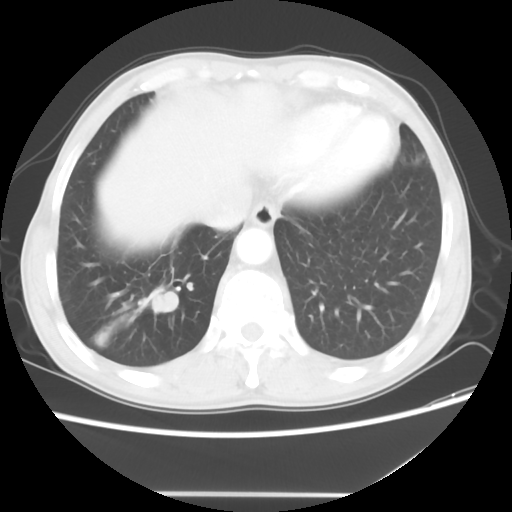
Chest CT, one axial slice; slice 10 of 56 in the series (ordered by position); 120 kVp; lung window (W 1500 / L -600 HU); 5 mm slice thickness; 512 × 512 image matrix, field of view 344 × 344 mm. Patient: male, 65 years. Case-level facts recorded for this patient, not image findings: clinical TNM (as recorded): T1c N3 M0.
Outlined on this slice (bounding box drawn by a radiologist):
- lung tumour (recorded histology: small cell carcinoma): bounding box (x1, y1, x2, y2) in pixels: (137, 279, 187, 321)